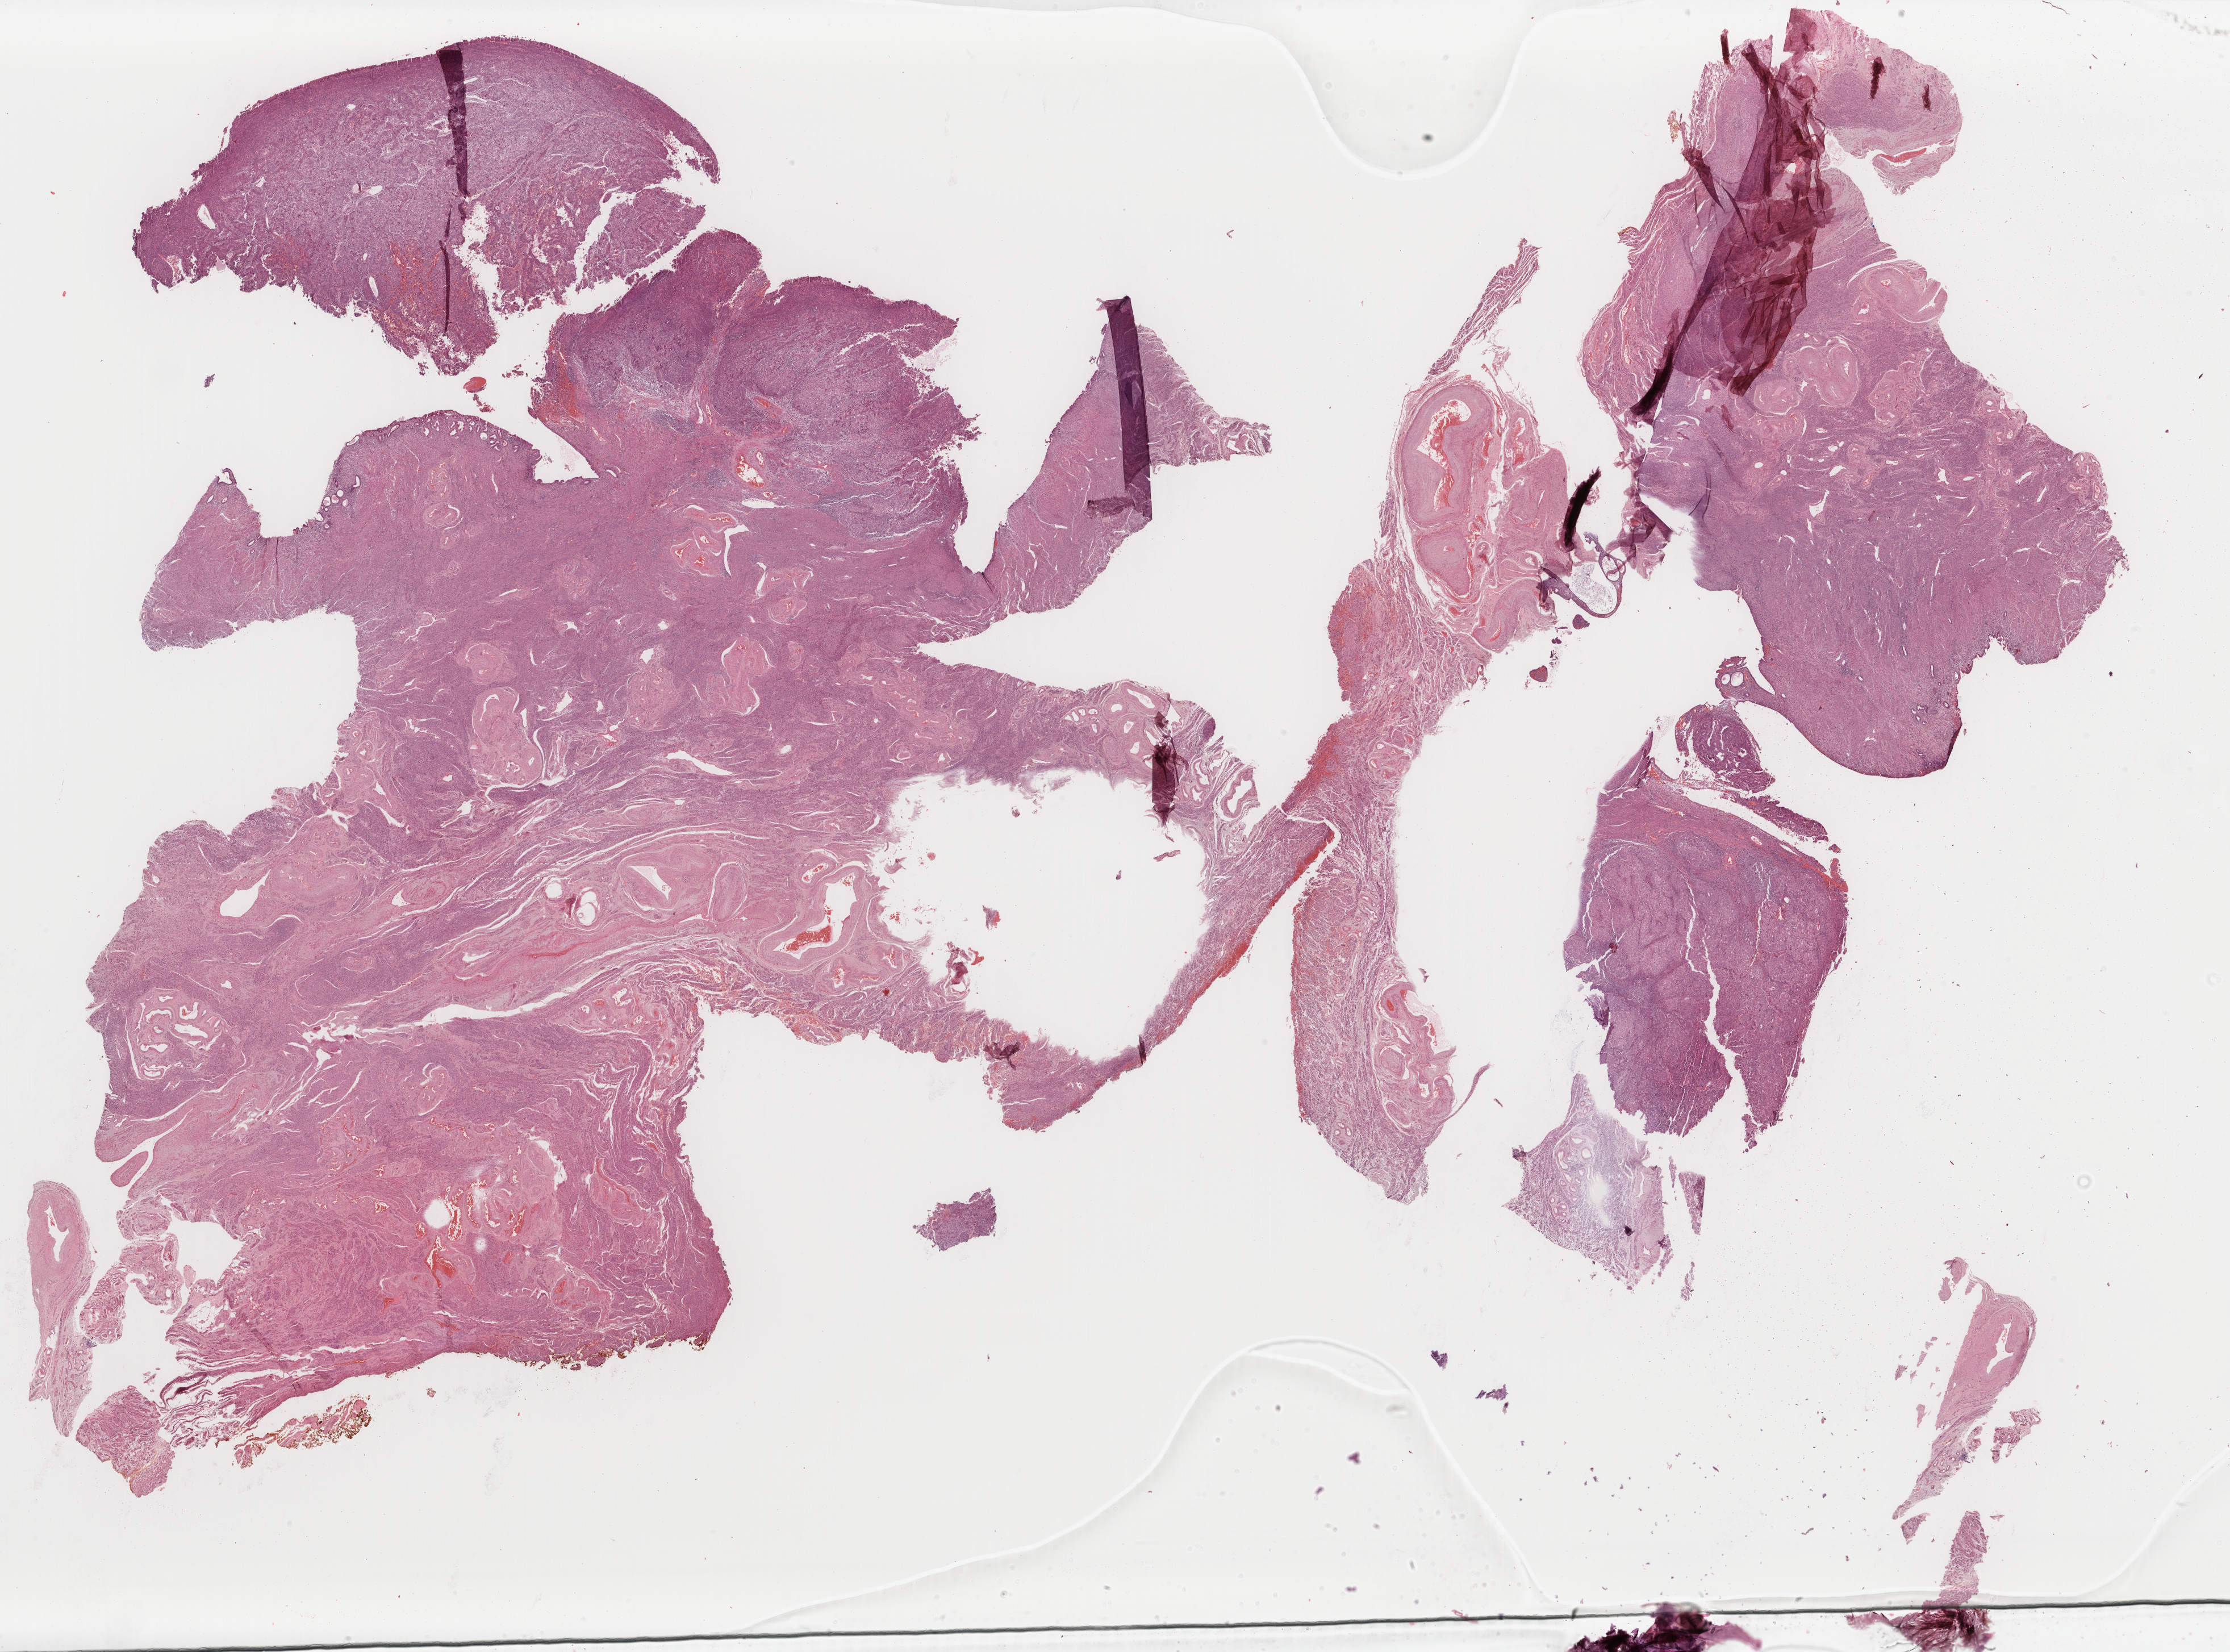
H&E-stained whole-slide image — whole scanned area (about 31.2 x 23.1 mm) shown as a low-resolution overview. Formalin-fixed paraffin-embedded (FFPE) diagnostic section. Sample: primary tumour, uterus. Patient: female, age at initial diagnosis 65 years. Histologic grade: G3 (poorly differentiated).
Diagnosis: Endometrioid adenocarcinoma, NOS (endometrium). FIGO stage: IB.